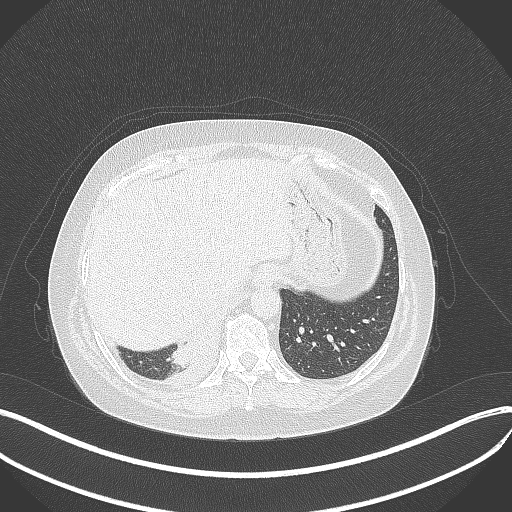
Chest CT, one axial slice; reconstruction kernel B70f; 120 kVp; lung window (W 1500 / L -600 HU); 1 mm slice thickness; 512 × 512 image matrix, field of view 400 × 400 mm. Female patient, age 56 years. Case-level facts recorded for this patient, not image findings: clinical TNM (as recorded): T2b N1 M0; histopathological grade: G3.
Annotated regions visible in this slice (bounding box drawn by a radiologist):
- lung tumour (recorded histology: small cell carcinoma): bounding box (x1, y1, x2, y2) in pixels: (173, 328, 219, 368)